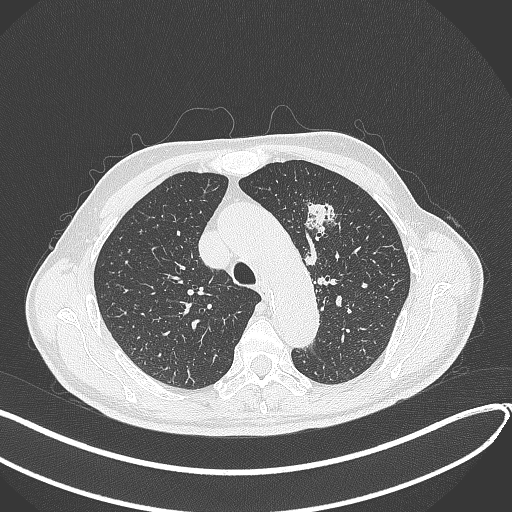
Chest CT, one axial slice. Position 306 of 459 along the scan axis. Reconstruction kernel B70f. Lung window (W 1500 / L -600 HU). 1 mm slice thickness. 512 × 512 image matrix. Patient: male, 74 years. From the clinical record (not read from this slice): clinical TNM (as recorded): T2b N0 M1c.
Annotated regions visible in this slice (bounding box drawn by a radiologist):
- lung tumour (recorded histology: adenocarcinoma): bounding box (x1, y1, x2, y2) in pixels: (303, 197, 339, 244)